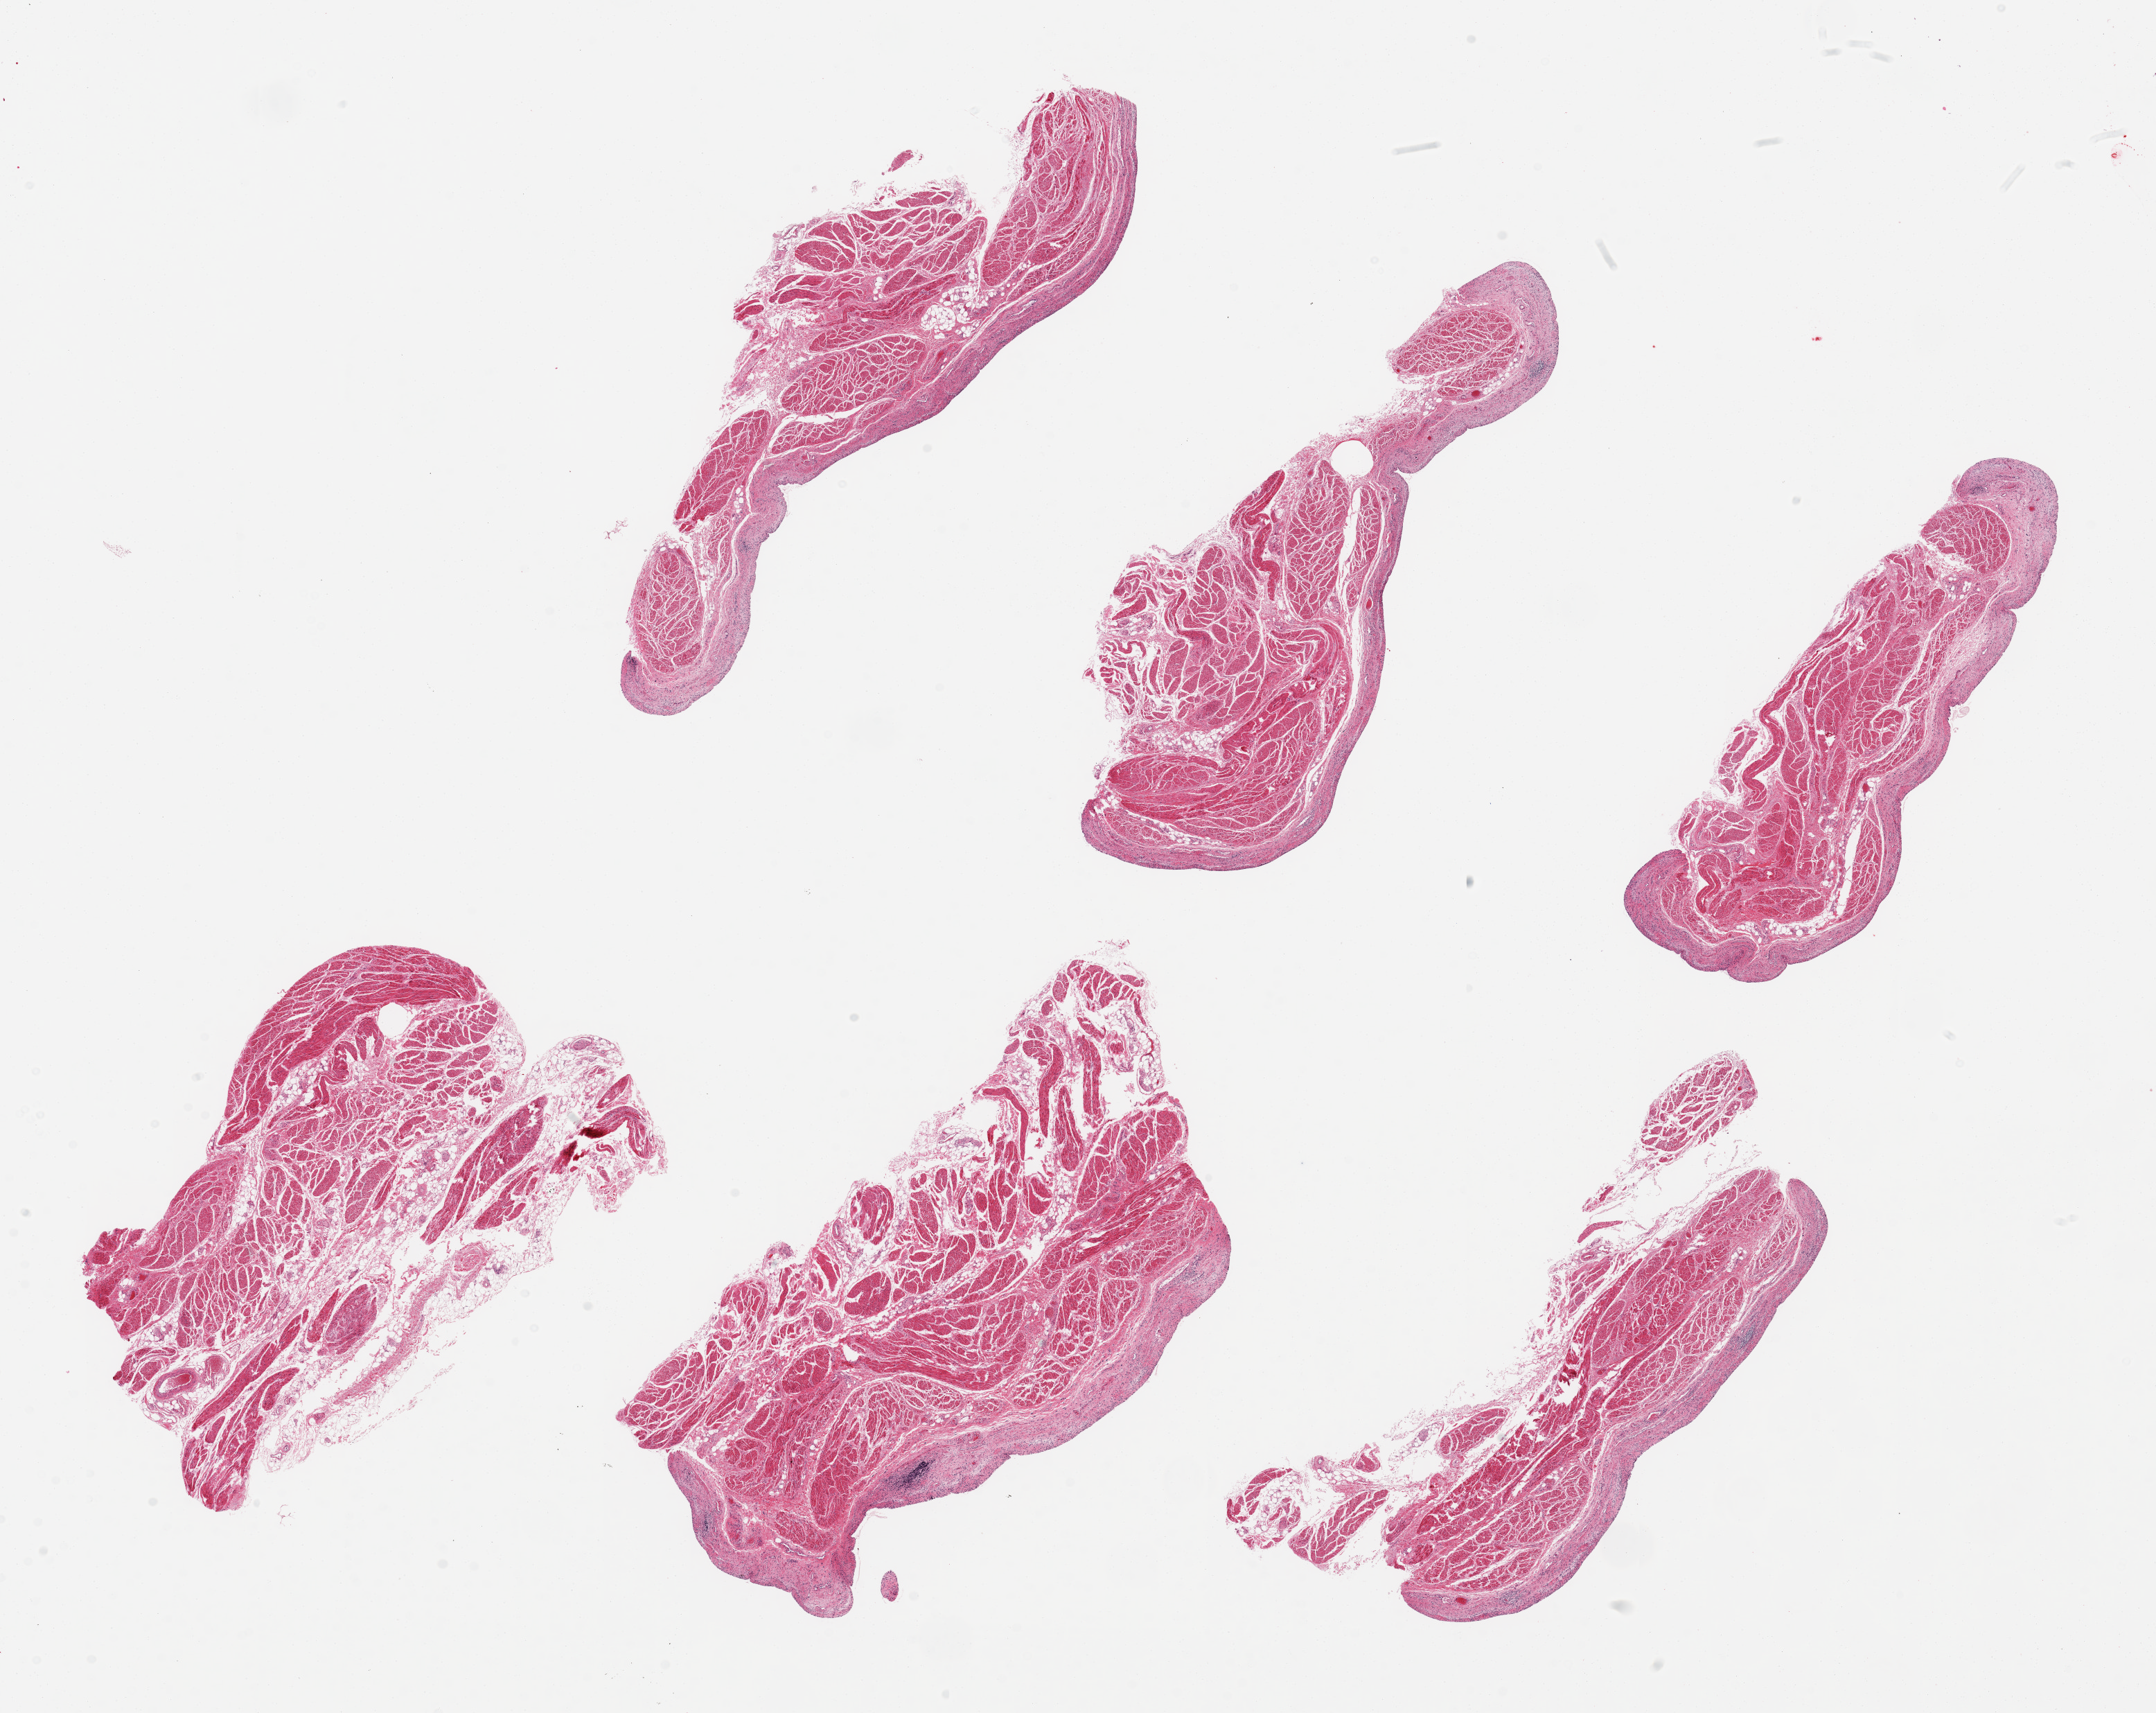
Digitized haematoxylin and eosin-stained section — shown as a low-resolution overview of the whole scanned area (about 24.6 x 19.5 mm, from a 20x scan); PAXgene-fixed paraffin-embedded (PFPE) section; target tissue: urinary bladder; donor tissue sample. Female donor.
Review note (as recorded): 6 pieces up to 9x4 mm; mucosa totally sloughed; muscle mild autolysis.